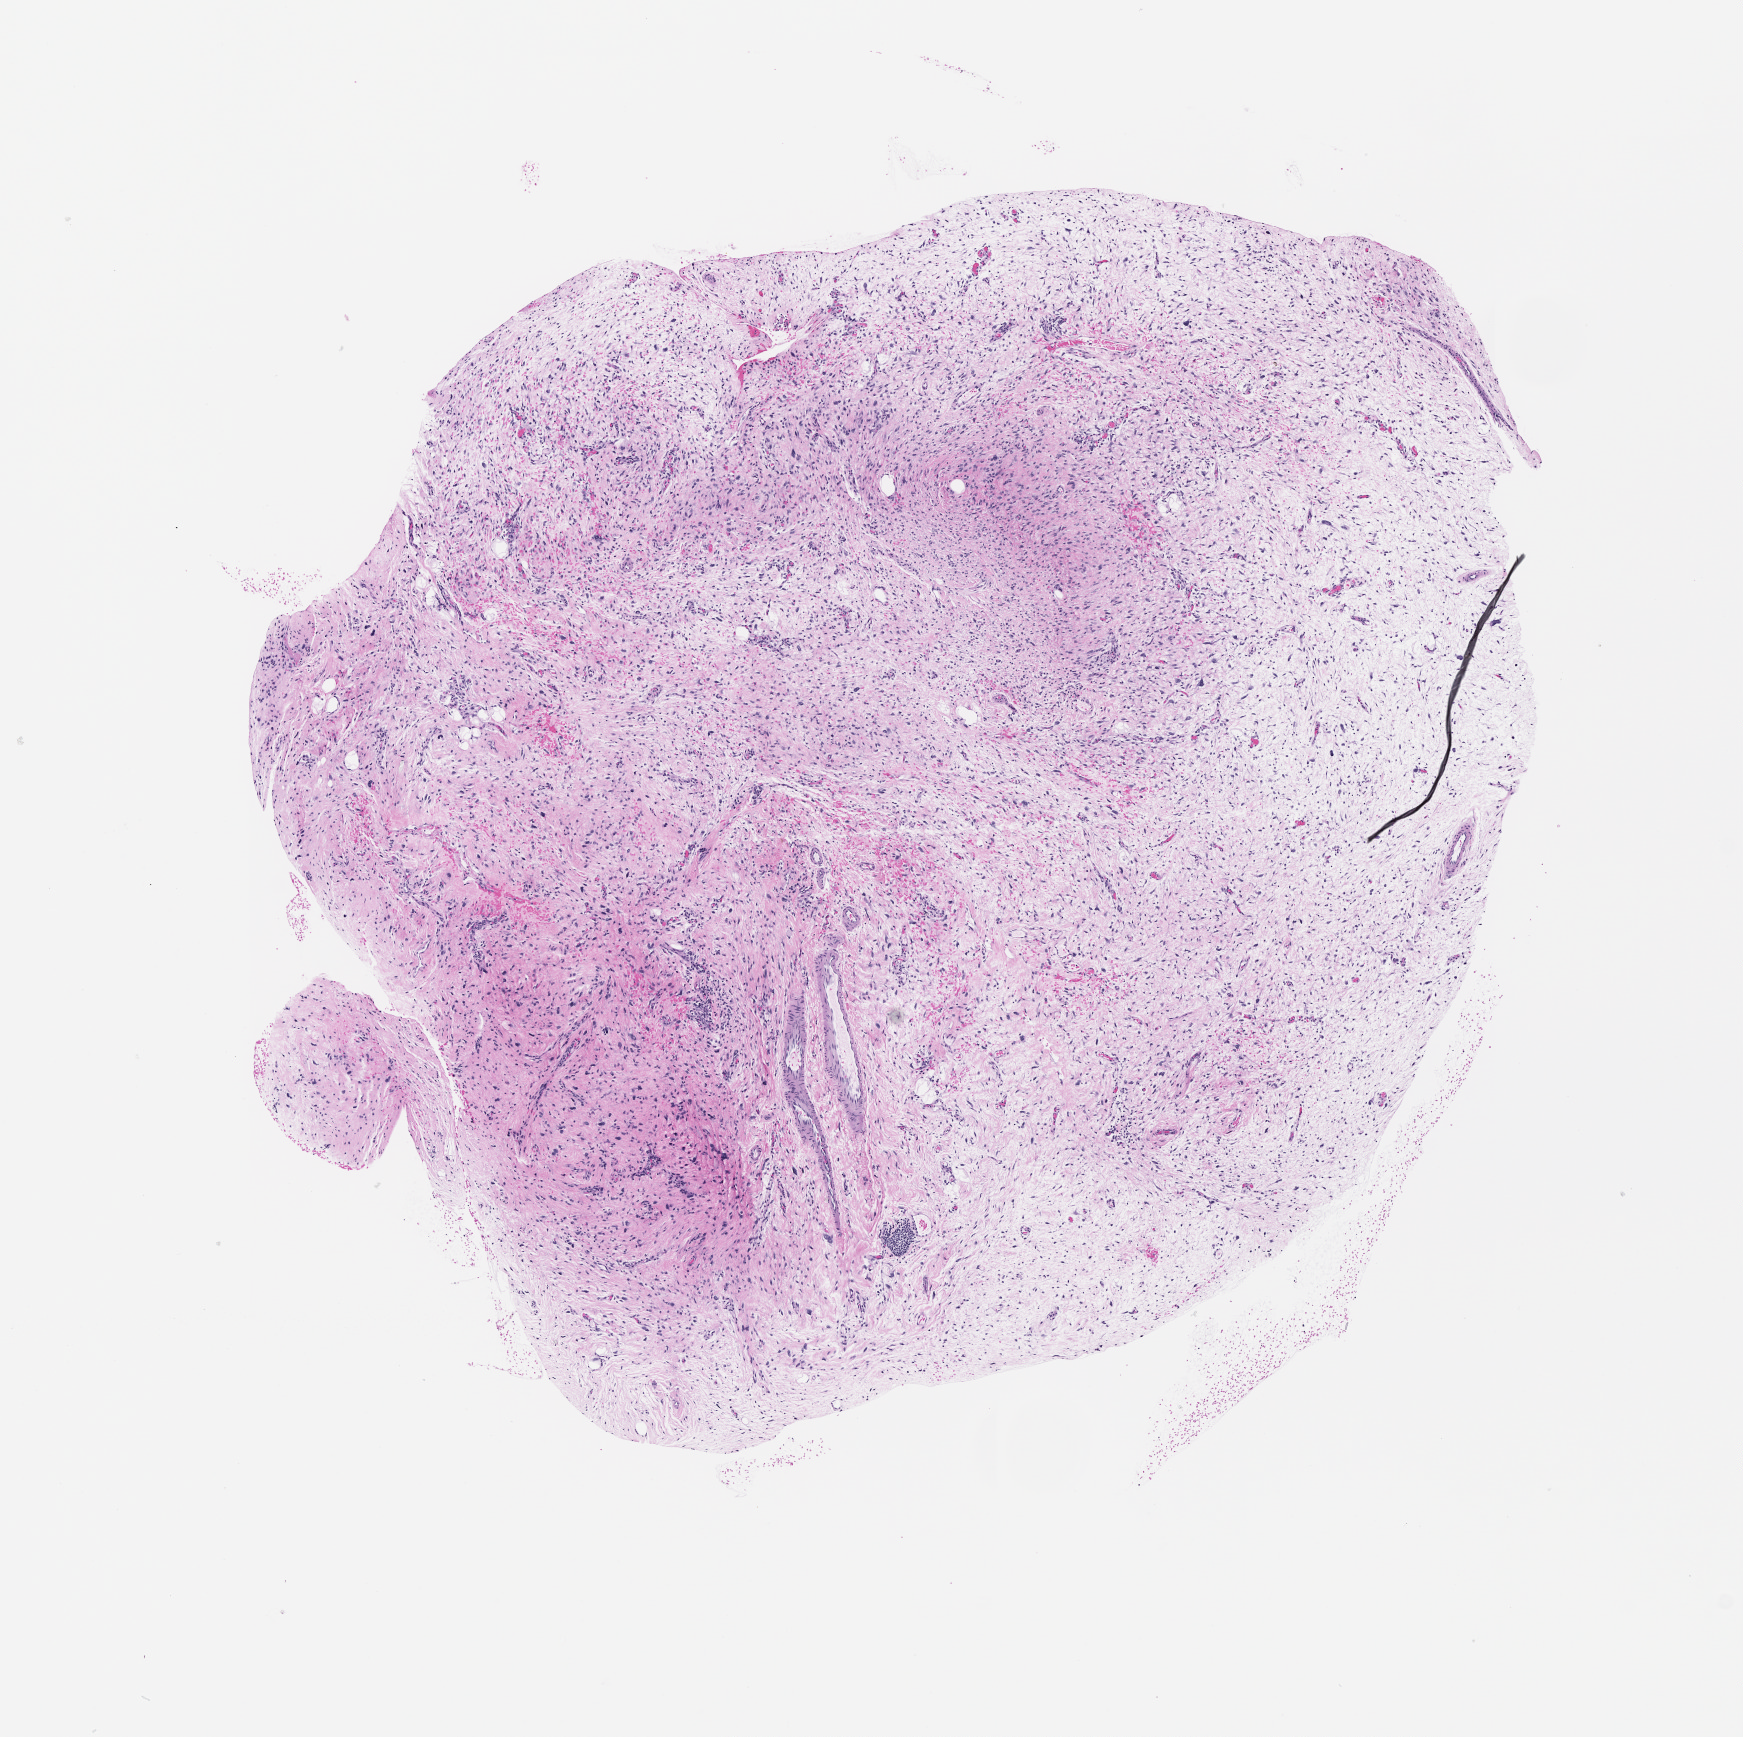
Whole-slide histology image, H&E-stained, low-resolution overview of the scanned area, about 7.0 x 7.0 mm.
Patient diagnosis (cohort enrolment): sarcoma (site not recorded at cohort level).